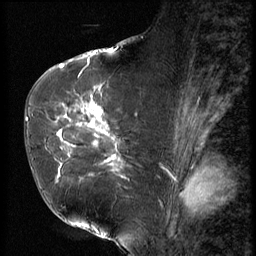
Breast MRI (dynamic contrast-enhanced), one sagittal slice; position 35 of 56 along the scan axis; 3 images stored at this slice position (order not interpretable as contrast timing); 1.5 T; TE 4.2 ms, TR 9 ms; 256 × 256 image matrix, field of view 180 × 180 mm. Female patient, age 61 years. From the clinical record (not read from this slice): setting: breast cancer imaged before/during neoadjuvant chemotherapy; receptor status: HR-positive, HER2-negative.
Structures marked on this image (semi-automatically segmented with operator editing):
- analysis volume of interest (the breast-tissue region the enhancement analysis was run in; not a lesion): box from (x=47, y=89) to (x=153, y=191) px
- tumour enhancement mask (voxels above the 140 % enhancement threshold inside the analysis volume of interest): (x=56, y=106)–(x=120, y=177)